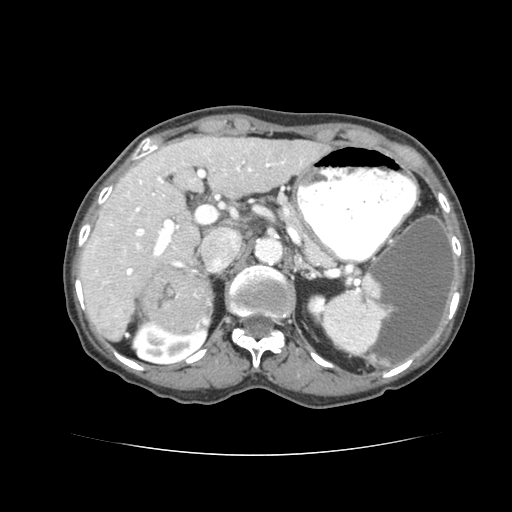
Contrast-enhanced abdominal CT (liver protocol), one axial slice; slice 45 of 77 in the series (ordered by position); 120 kVp; soft-tissue window (W 400 / L 40 HU); 512 × 512 image matrix, field of view 340 × 340 mm. From the clinical record (not read from this slice): diagnosis: hepatocellular carcinoma (patient treated with transarterial chemoembolisation; whether this scan precedes or follows treatment is not stated here); TNM stage (as recorded): Stage-I; Child-Pugh class: A; tumour differentiation: well differentiated; tumour nodularity: uninodular.
Outlined on this slice (semi-automatically segmented with operator editing):
- liver parenchyma outside the tumour (the mass and vessels are separate outlines, so this box may not span the whole liver): bounding box [x1, y1, x2, y2] px = [78, 134, 328, 336]
- mass: [140, 263, 212, 332]
- liver vessels: [81, 147, 284, 307]